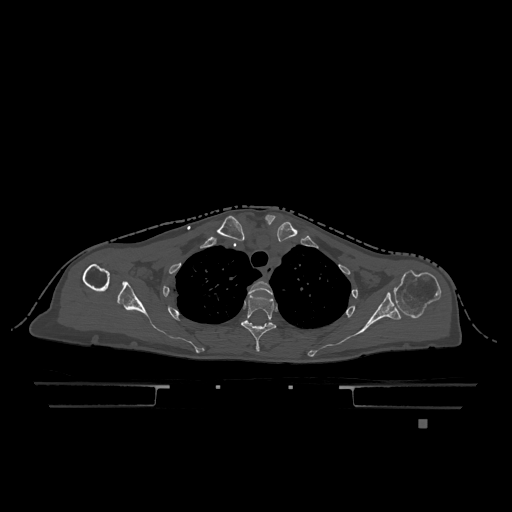
CT including the spine, one axial slice; position 925 of 1317 along the scan axis; bone window (W 1800 / L 400 HU); 0.5 mm slice thickness; 512 × 512 image matrix, field of view 500 × 500 mm. Patient: female, 74 years. Case-level facts recorded for this patient, not image findings: primary cancer: lung; vertebrae with lytic lesions (as recorded): T1, T4, T5, T6, L4, L5.
Structures marked on this image (semi-automatically segmented with operator editing):
- T2 vertebra: box from (x=248, y=281) to (x=273, y=295) px
- T3 vertebra: (x=241, y=295)–(x=276, y=352)